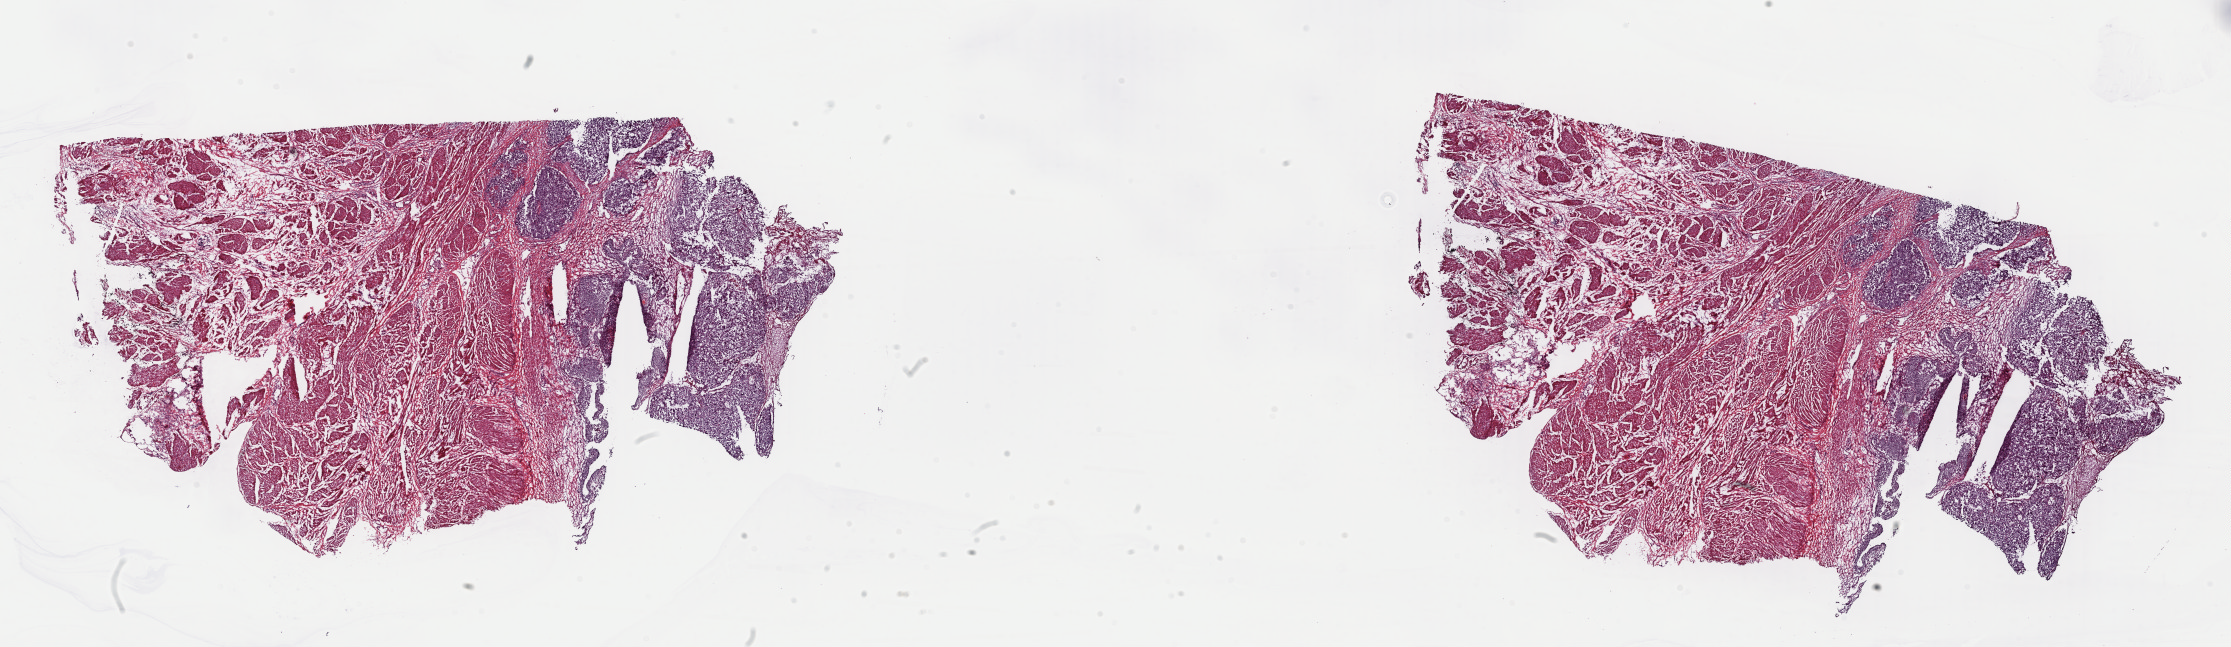
H&E-stained whole-slide image, shown as a low-resolution overview of the whole scanned area (about 35.2 x 10.2 mm). Frozen section. Sample: primary tumour, bladder. Male patient; age at initial diagnosis 82 years. Histologic grade: high grade. Slide review estimates, as recorded: tumour cells 70%, tumour nuclei 70%, normal cells 0%, stromal cells 24%, necrosis 6%. Inflammatory infiltration, as recorded: lymphocyte infiltration 5%, monocyte infiltration 2%, neutrophil infiltration 3%.
AJCC pathologic stage: IV (7th edition). Diagnosis: Transitional cell carcinoma (posterior wall of bladder). Lymph nodes positive (case pathology): 1 of 8 examined.